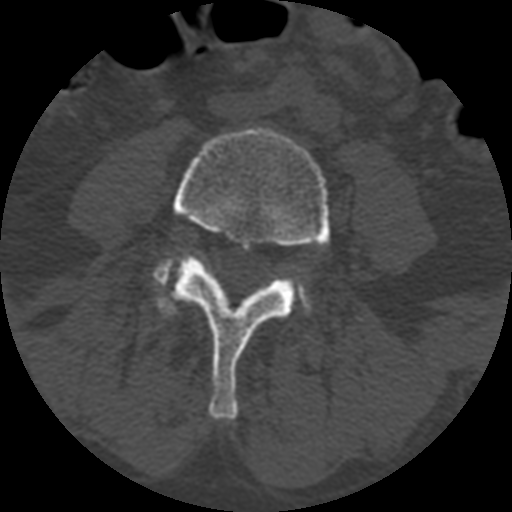
CT including the spine, one axial slice. Slice 278 of 399 in the series (ordered by position). Reconstruction kernel STANDARD. Bone window (W 1800 / L 400 HU). 1.25 mm slice thickness. 512 × 512 image matrix, field of view 160 × 160 mm. Patient age 71 years. From the clinical record (not read from this slice): primary cancer: prostate.
Structures marked on this image (semi-automatically segmented with operator editing):
- L4 vertebra: bounding box (x1, y1, x2, y2) in pixels: (162, 128, 330, 420)
- L5 vertebra: (154, 257, 311, 311)